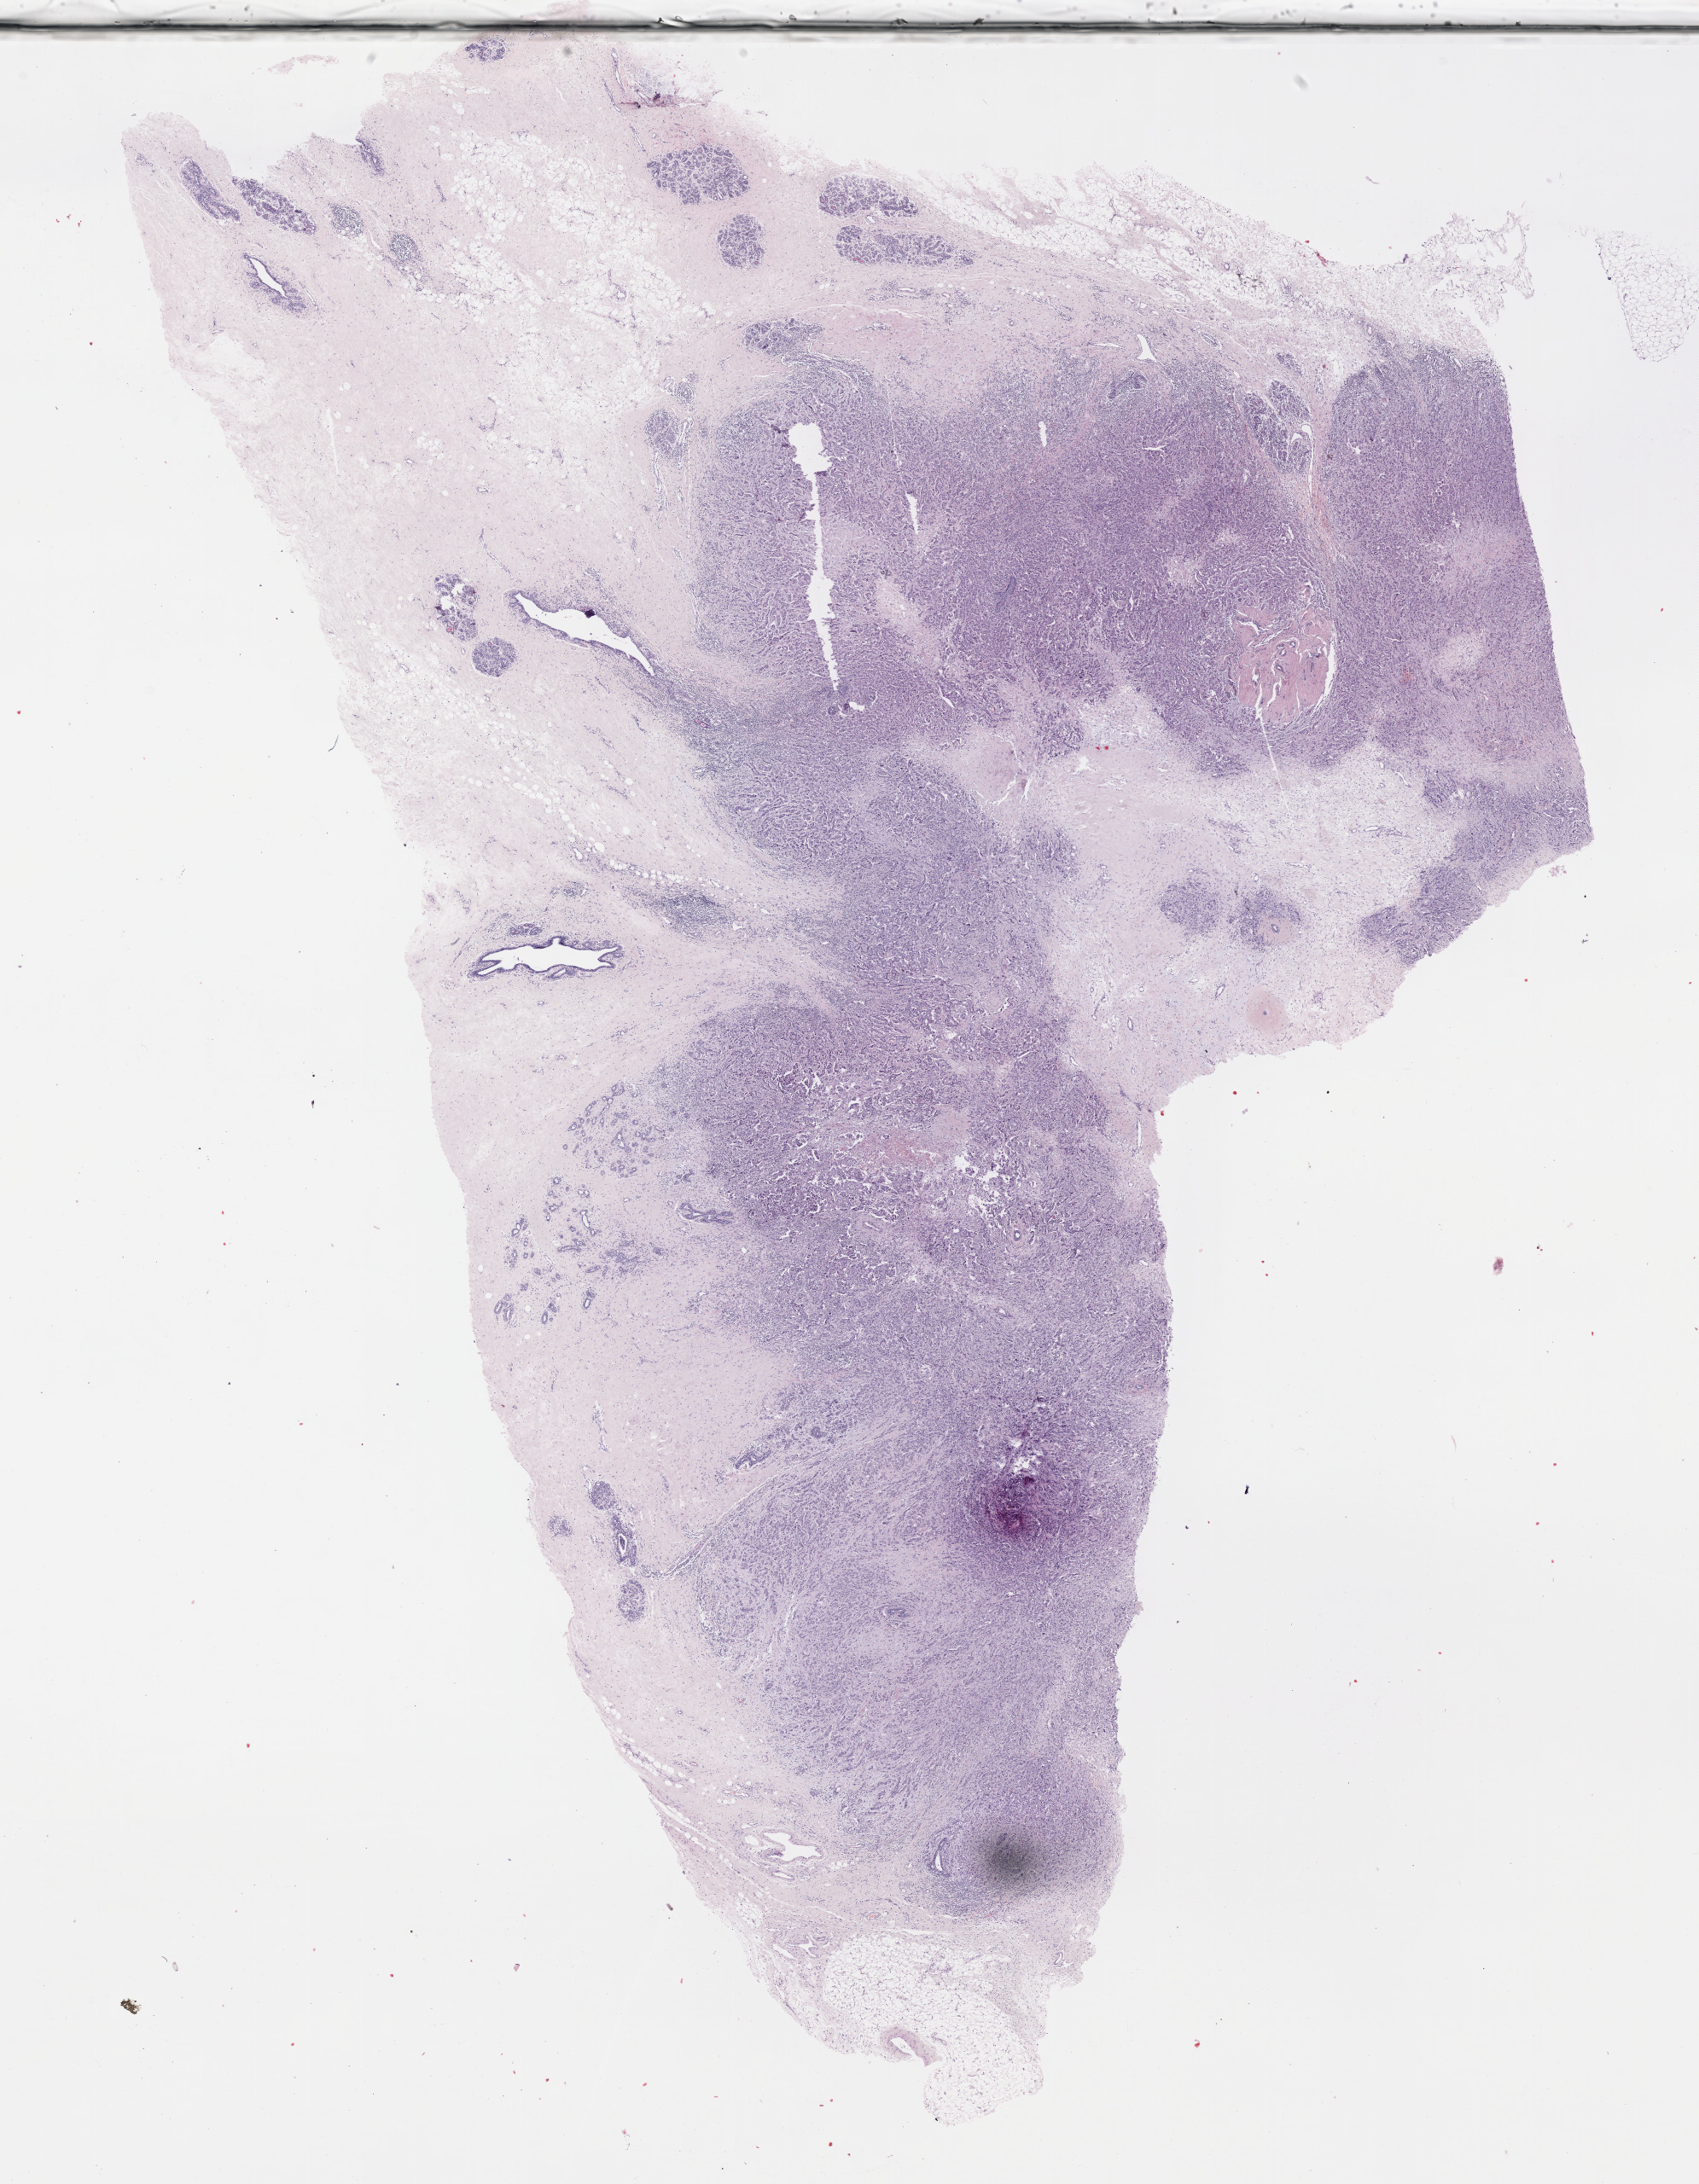
Hematoxylin and eosin (H&E) stained whole-slide image — low-resolution overview of the scanned area, about 16.1 x 20.7 mm (from a 40x scan); formalin-fixed paraffin-embedded (FFPE) diagnostic section; breast, primary tumour sample. Patient: female, age at initial diagnosis 48 years.
- AJCC pathologic stage: IA
- lymph nodes positive (case pathology): 0 of 6 examined
- laterality: left
- diagnosis: Infiltrating duct carcinoma, NOS